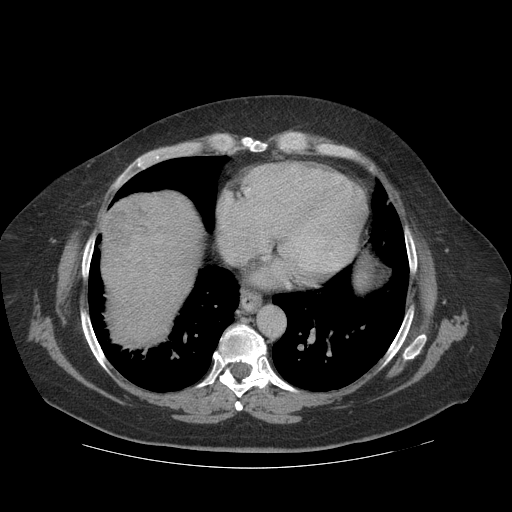
Contrast-enhanced abdominal CT (liver protocol), one axial slice; position 106 of 121 along the scan axis; reconstruction kernel STANDARD; 140 kVp; soft-tissue window (W 400 / L 40 HU); 512 × 512 image matrix, field of view 420 × 420 mm. Case-level facts recorded for this patient, not image findings: diagnosis: hepatocellular carcinoma (patient treated with transarterial chemoembolisation; whether this scan precedes or follows treatment is not stated here); TNM stage (as recorded): Stage-IIIA; Child-Pugh class: A; tumour differentiation: well differentiated; tumour nodularity: multinodular.
Outlined on this slice (semi-automatic segmentation, software-assisted and operator-edited):
- liver parenchyma outside the tumour (the mass and vessels are separate outlines, so this box may not span the whole liver): bounding box [x1, y1, x2, y2] px = [100, 192, 200, 342]
- mass: [99, 200, 162, 247]